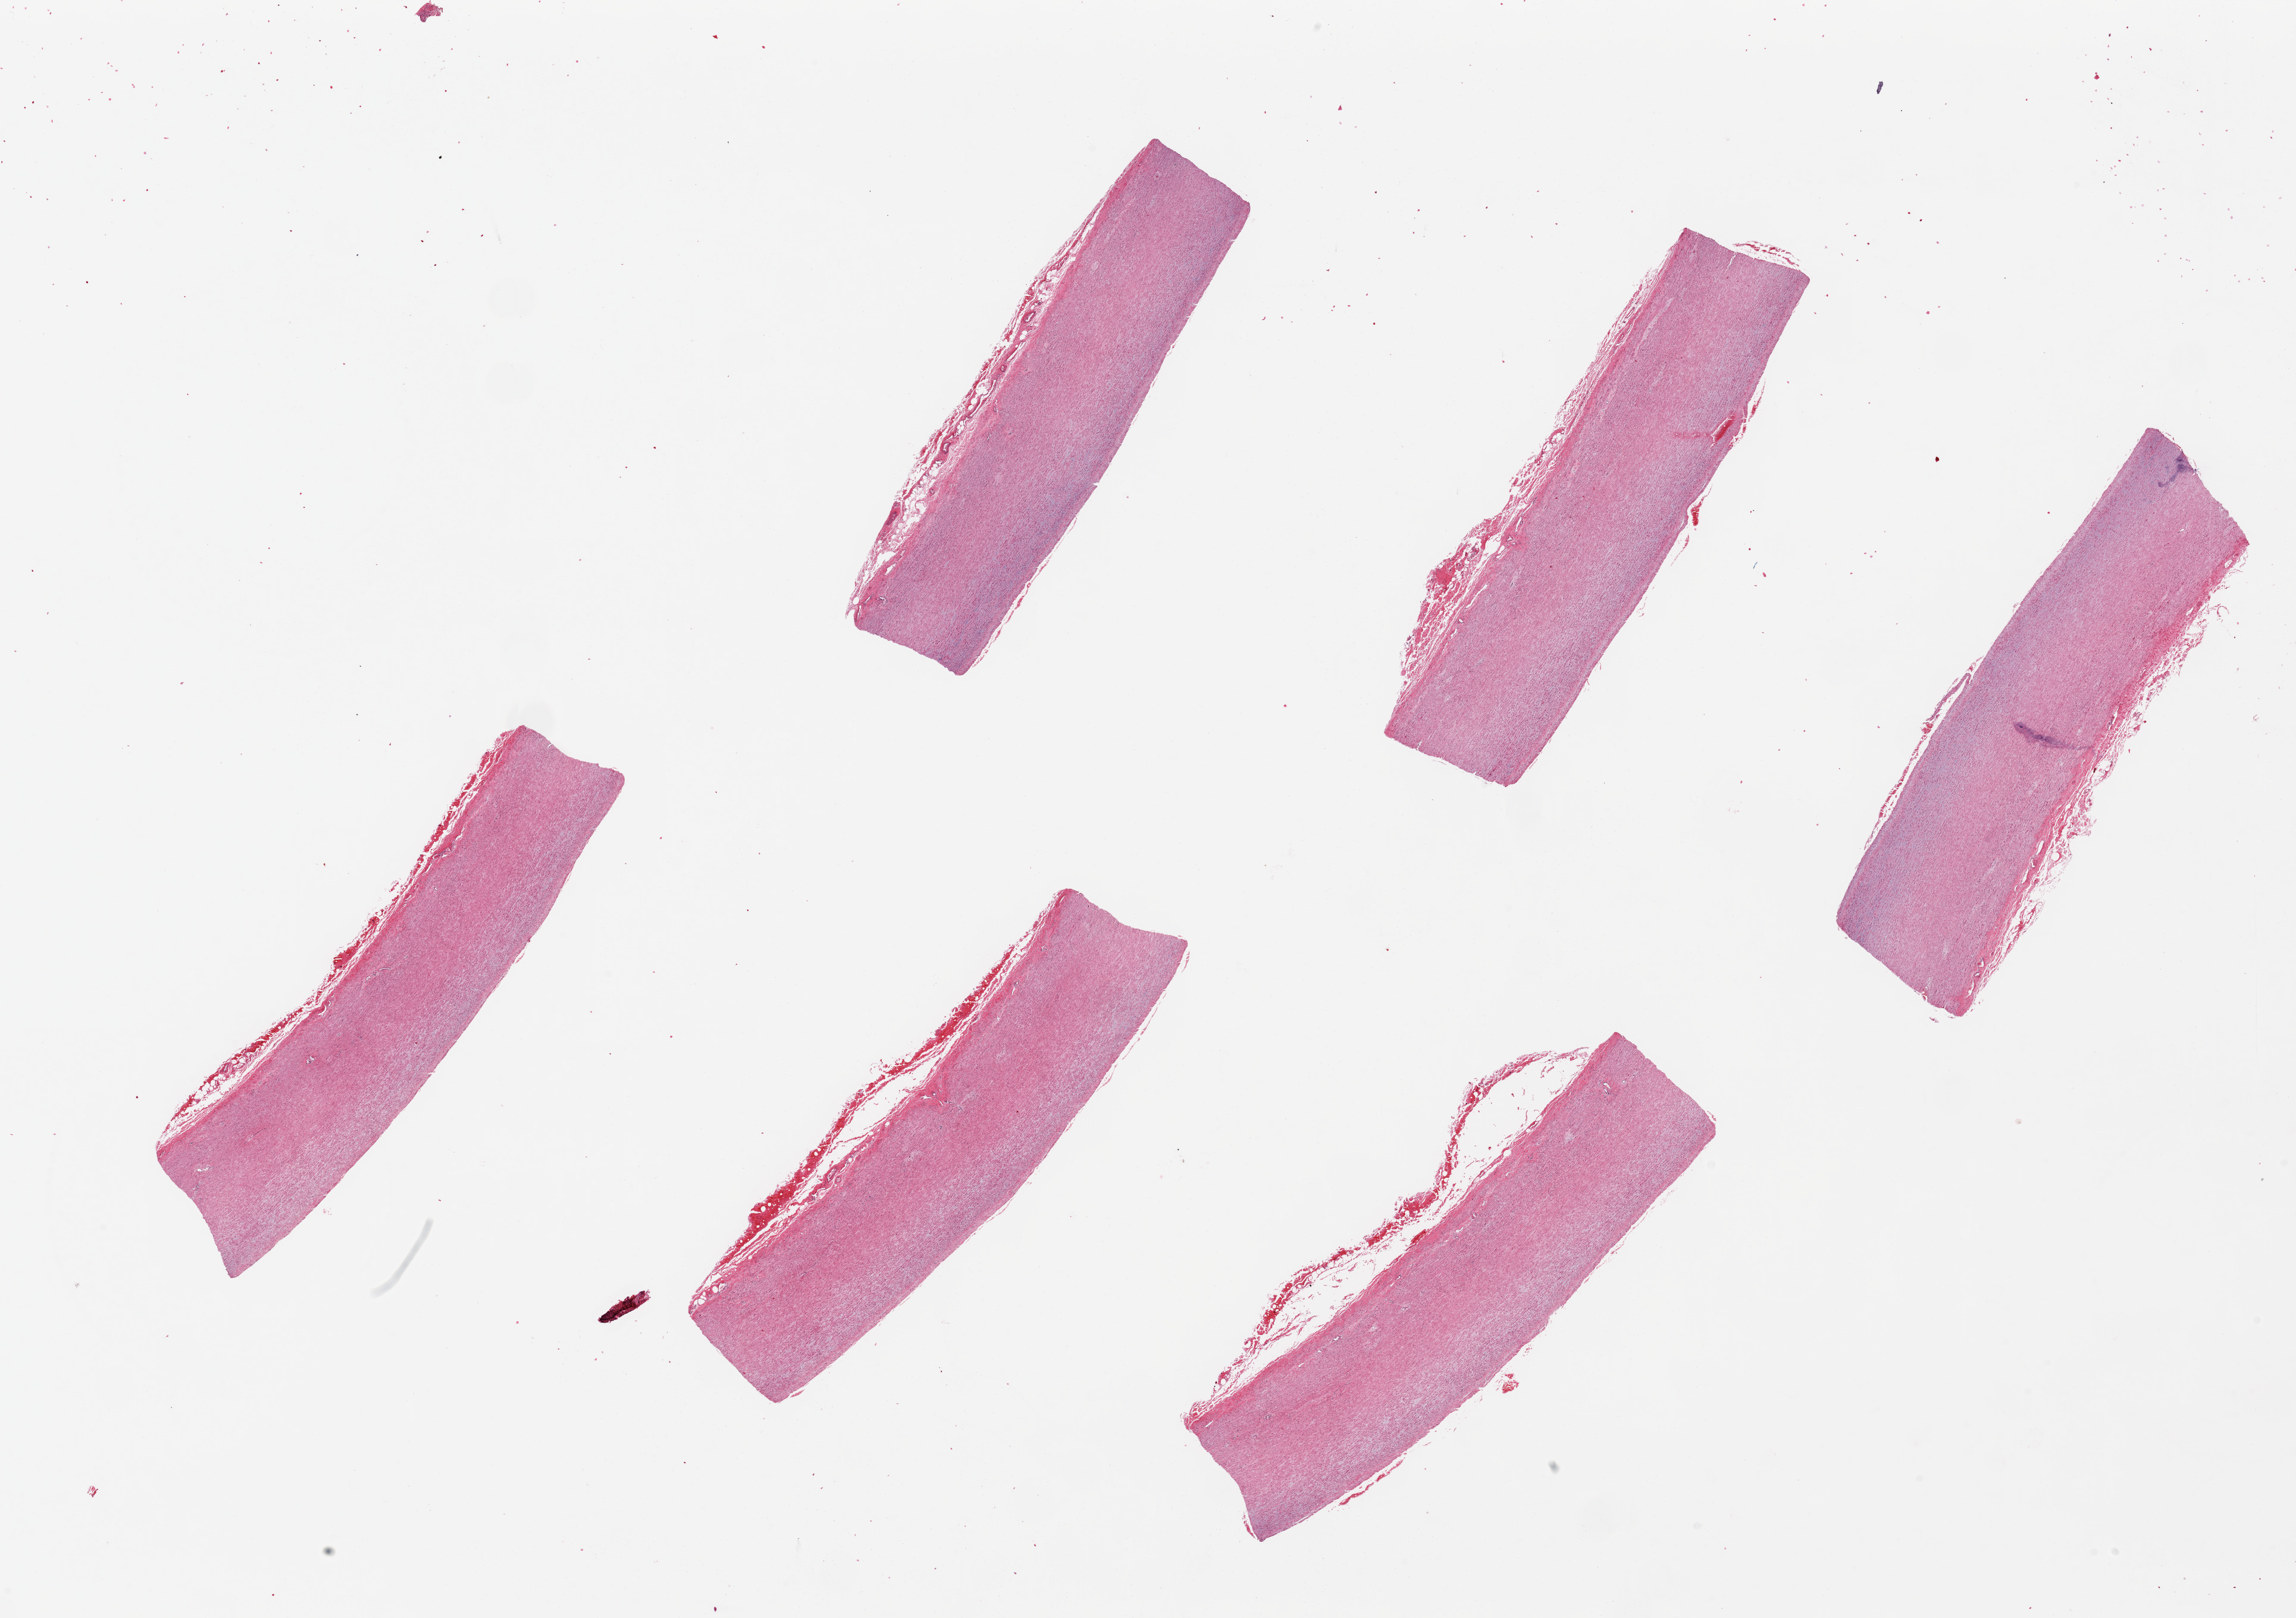
Whole-slide image, hematoxylin and eosin (H&E) stain, brightfield — low-resolution overview of the scanned area, about 30.5 x 21.5 mm (from a 20x scan); PAXgene-fixed paraffin-embedded (PFPE) section; sampled site (target tissue): aorta; donor tissue sample. Female donor.
Review note (as recorded): 6 pieces, ~8x2mm.